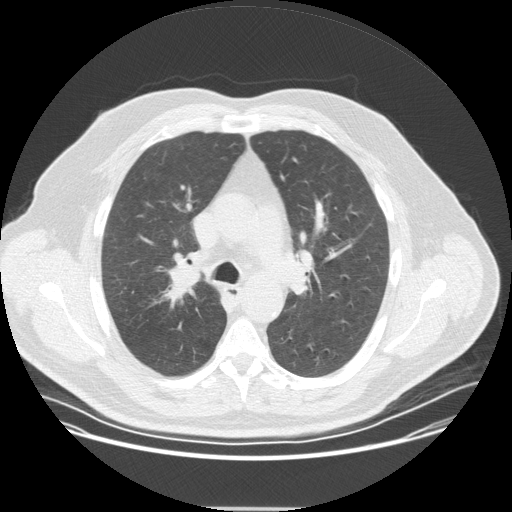
Low-dose screening chest CT, one axial slice. Position 232 of 351 along the scan axis. Lung window (W 1500 / L -600 HU). 2.5 mm slice thickness. 512 × 512 image matrix.
Annotated regions visible in this slice (expert manual segmentation):
- lesion 1 (tumor, upper lobe of right lung): bounding box [x1, y1, x2, y2] px = [163, 266, 202, 304]